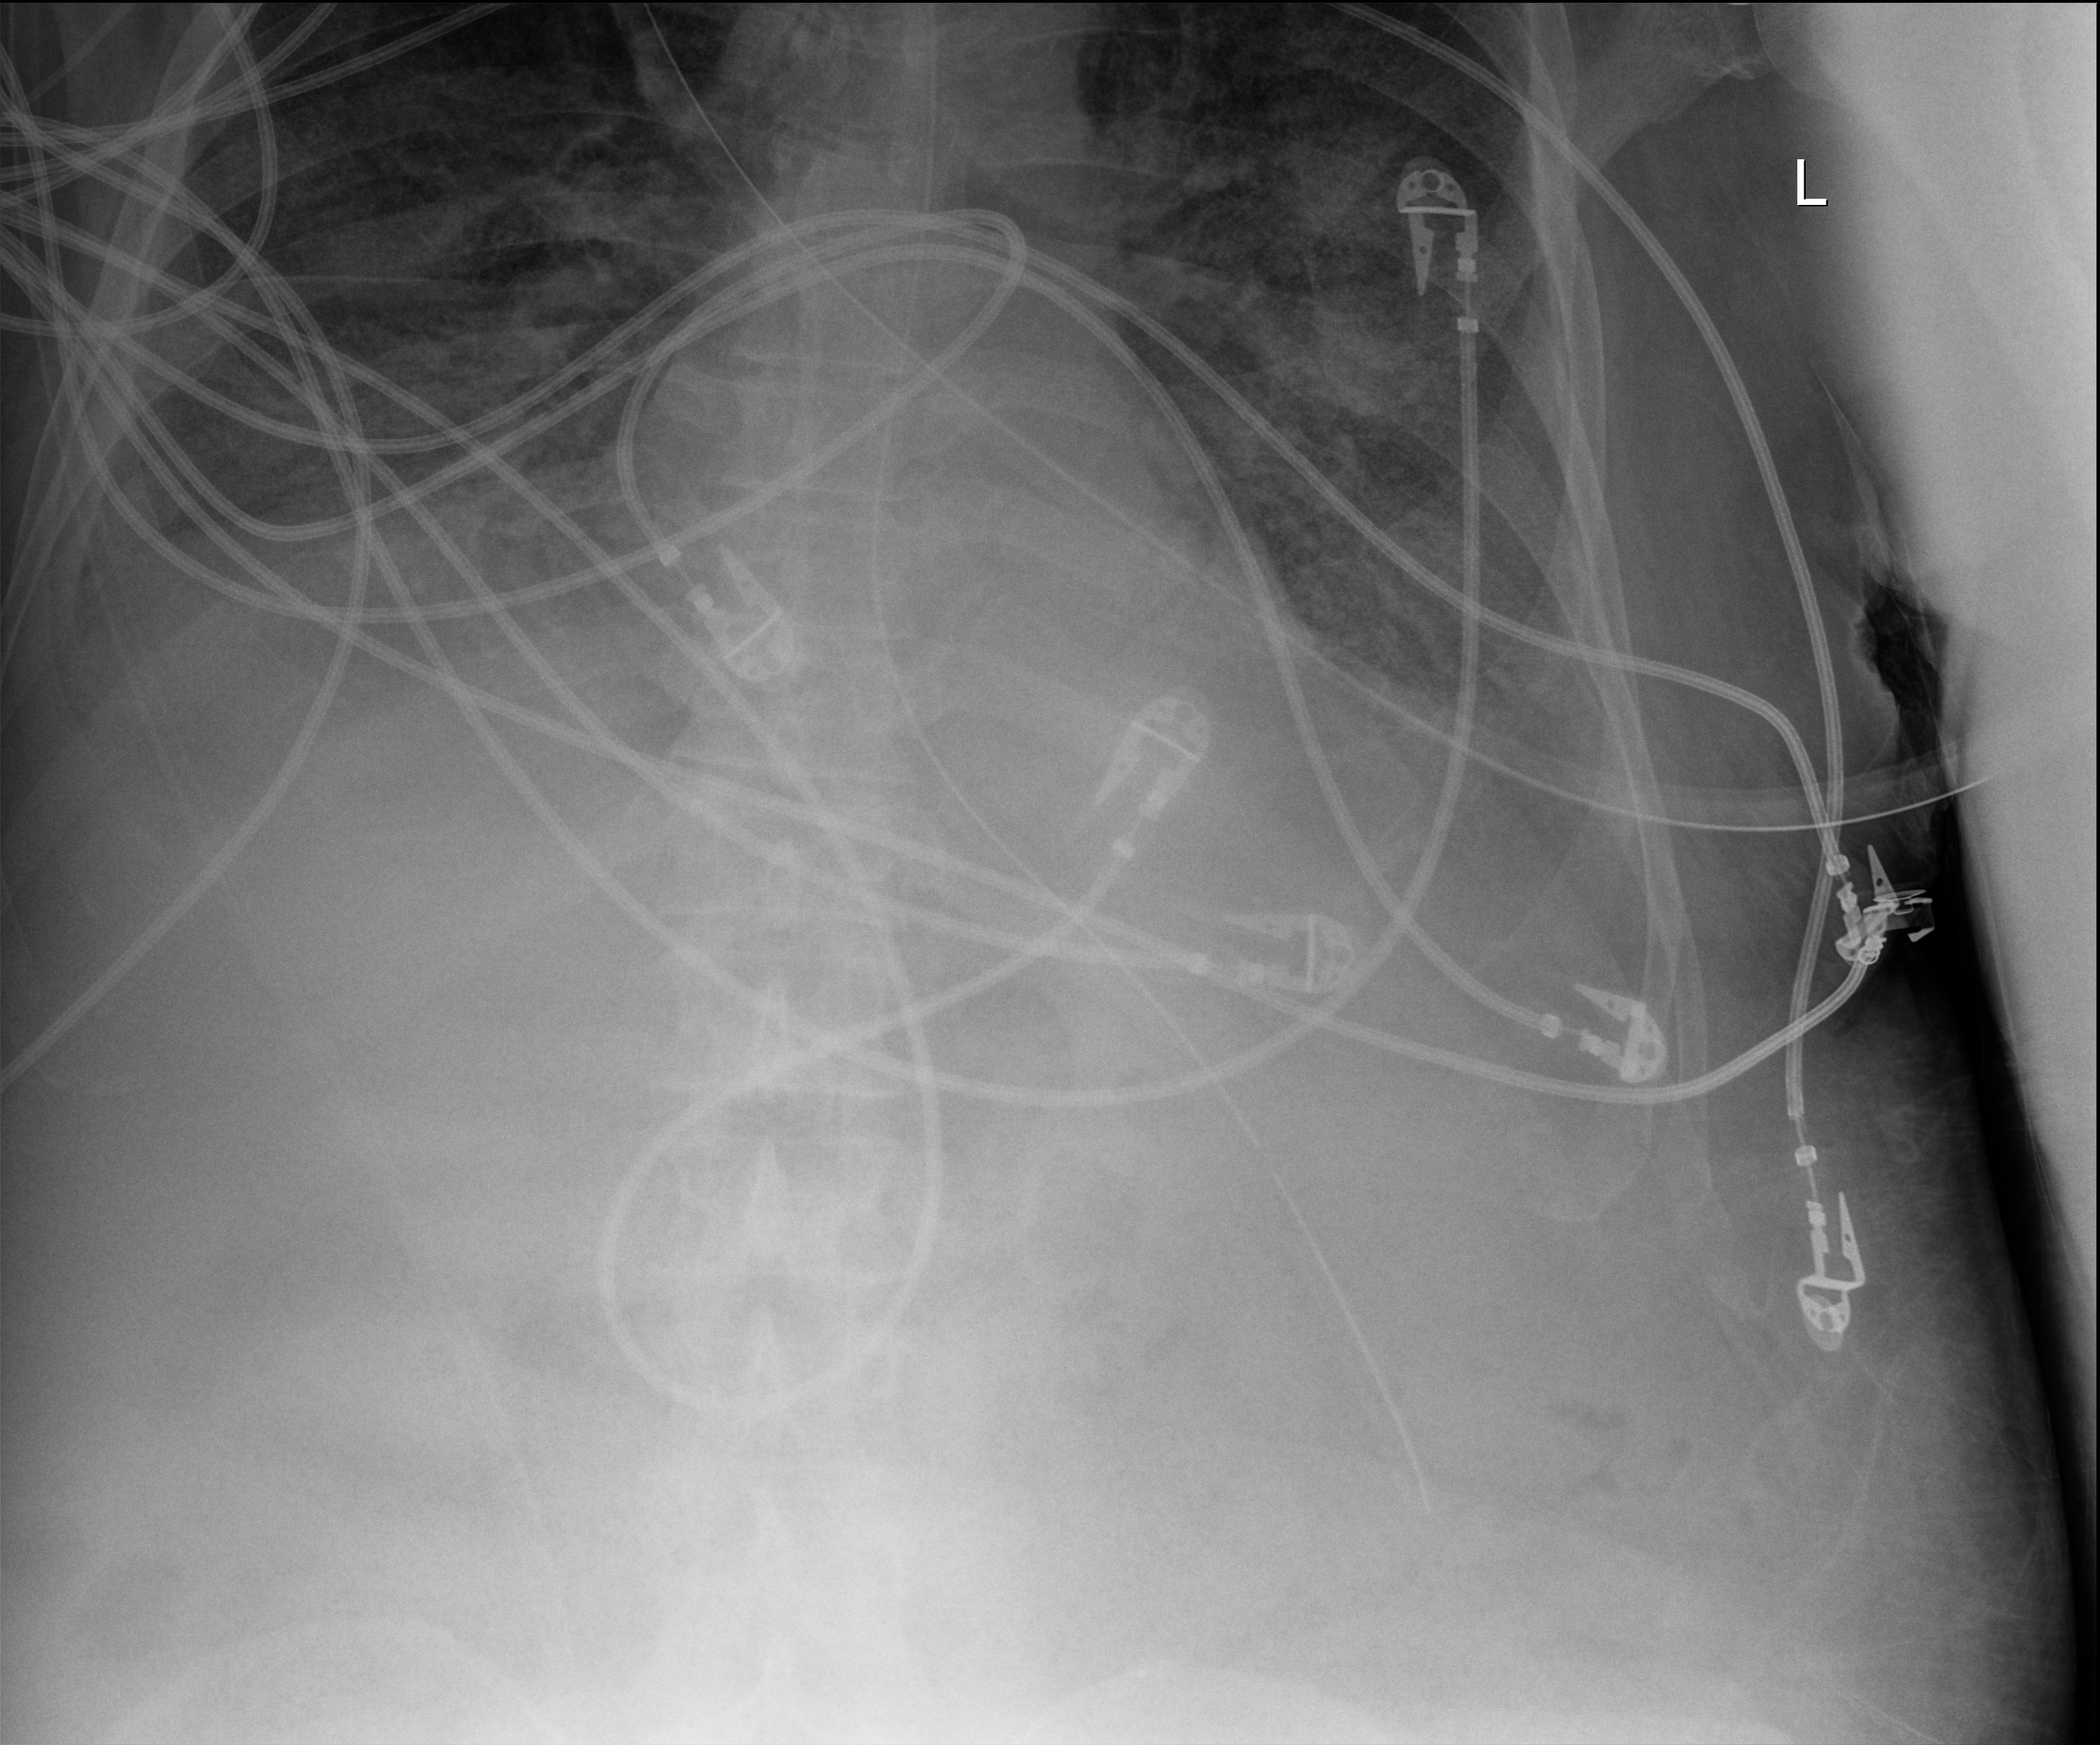
Portable chest radiograph, anteroposterior (AP) projection. Patient hospitalised with COVID-19; male, aged 60–74 years.
Hospital-stay facts (about this admission, not read from this image; timing relative to this image not recorded): other chronic lung disease (admission record): no; admitted to intensive care during this hospital stay: yes; mechanically ventilated during this hospital stay: yes.